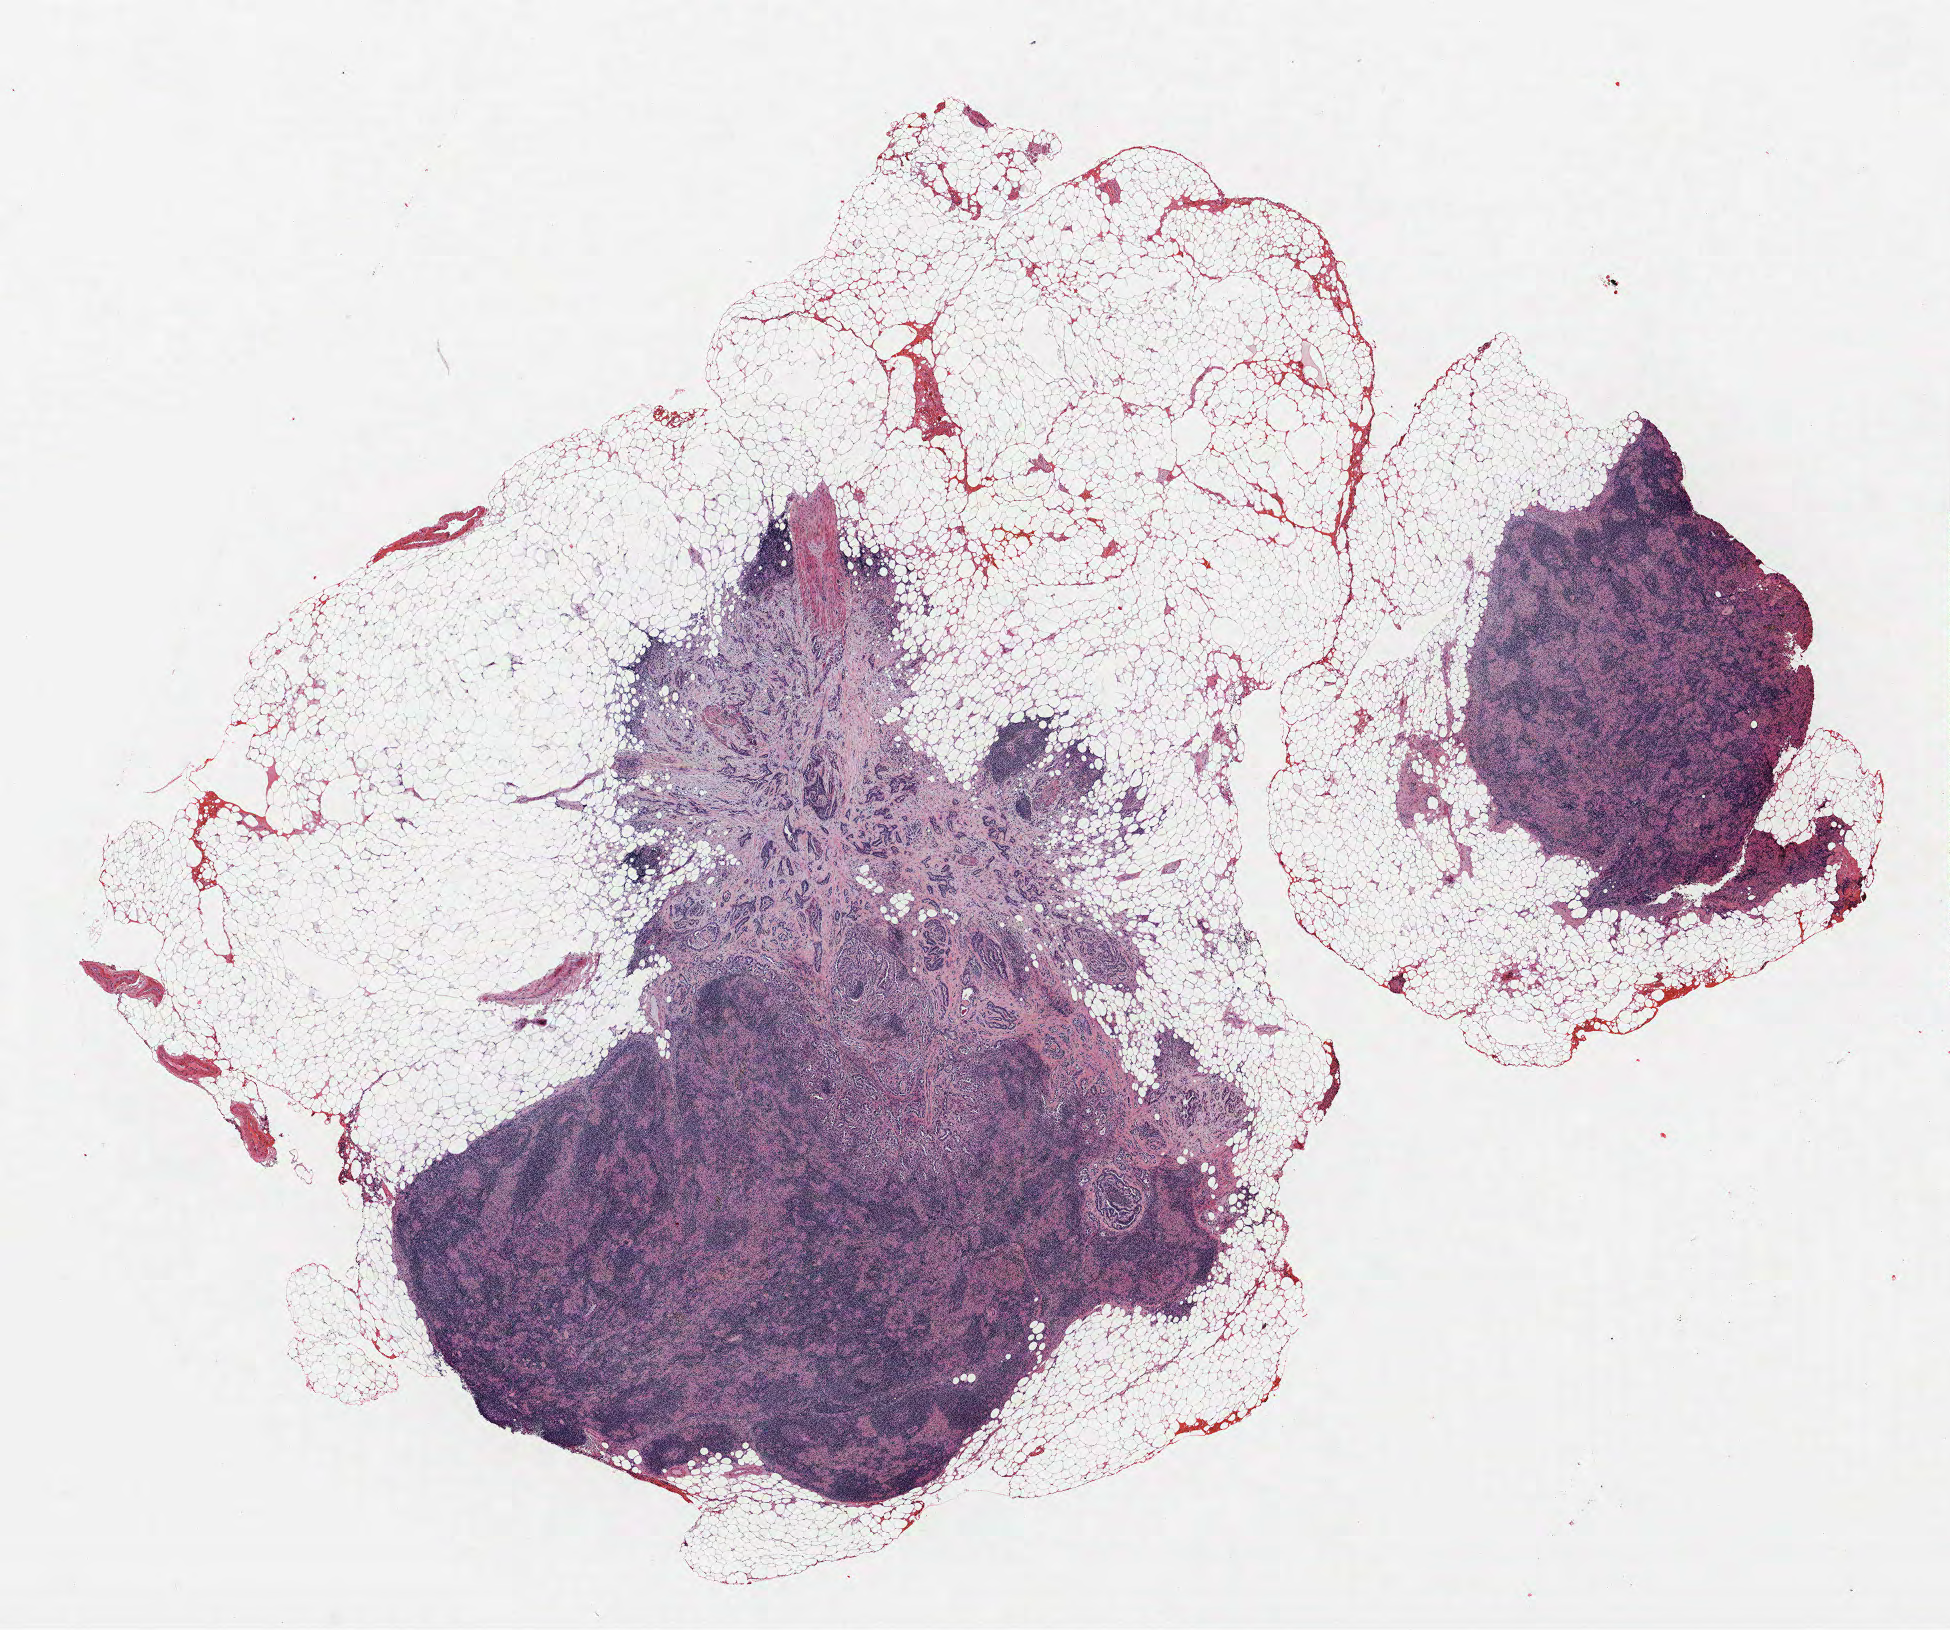
Hematoxylin and eosin (H&E) stained whole-slide image, a low-resolution overview of the entire scanned area, about 15.6 x 13.0 mm (slide scanned at 40x). FFPE section. Lung. Male, age 66 at enrolment. Former smoker at enrolment. Grade: poorly differentiated (G3).
• primary tumour location (clinical record): right upper lobe
• tumour size (pathology): 33 mm
• stage (AJCC 6th edition): IIB
• participant's lung-cancer diagnosis: Adenocarcinoma, NOS
• ICD-O-3 topography: upper lobe of lung (C34.1)